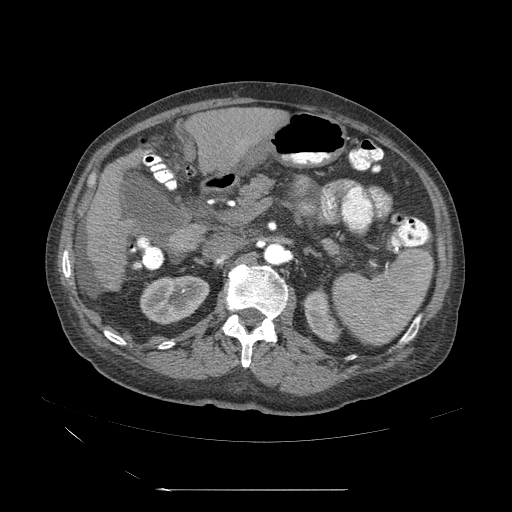
Contrast-enhanced abdominal CT (liver protocol), one axial slice. Slice 19 of 71 in the series (ordered by position). 120 kVp. Soft-tissue window (W 400 / L 40 HU). 2.5 mm slice thickness. 512 × 512 image matrix. From the clinical record (not read from this slice): diagnosis: hepatocellular carcinoma (patient treated with transarterial chemoembolisation; whether this scan precedes or follows treatment is not stated here); TNM stage (as recorded): Stage-II; Child-Pugh class: A; tumour nodularity: multinodular; tumour size: 1 cm.
Structures marked on this image (semi-automatic segmentation, software-assisted and operator-edited):
- abdominal aorta: bounding box [x1, y1, x2, y2] px = [263, 243, 286, 268]
- liver parenchyma outside the tumour (the mass and vessels are separate outlines, so this box may not span the whole liver): [84, 179, 166, 294]